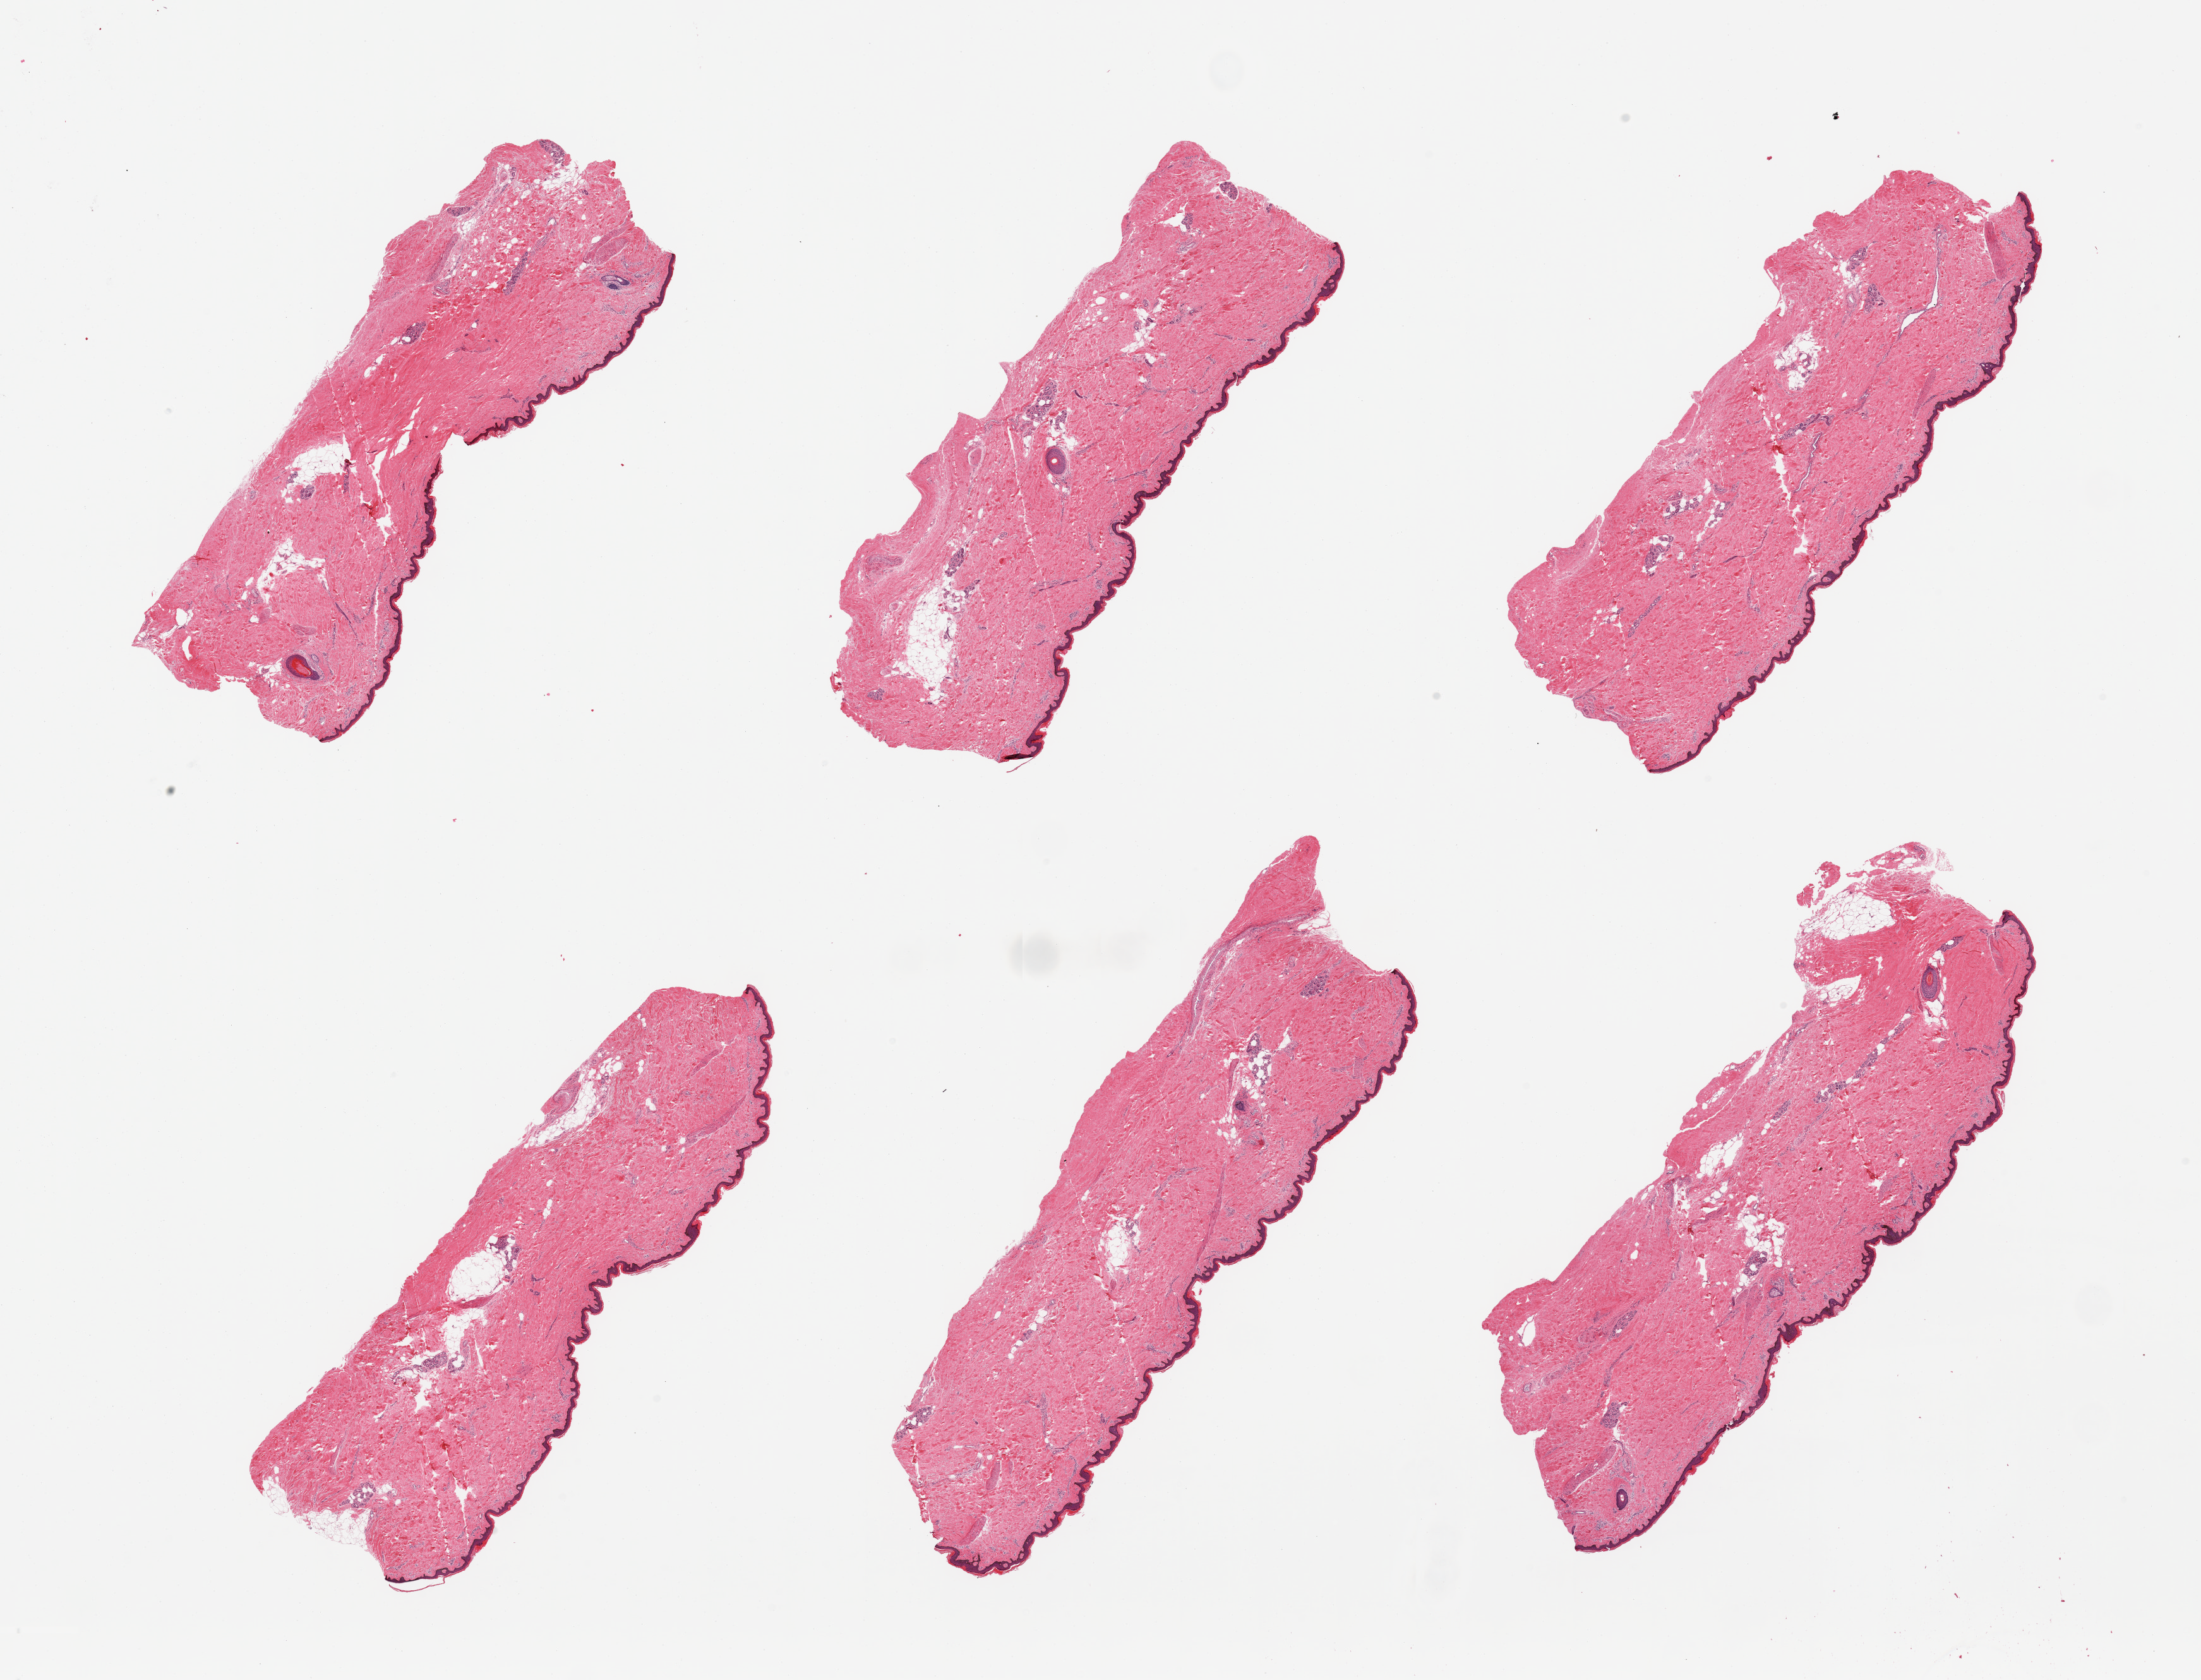
Whole-slide image, haematoxylin and eosin stain, brightfield, shown as a low-resolution overview of the whole scanned area (about 27.6 x 21.0 mm, acquisition: 20x scan). PAXgene-fixed, paraffin-embedded tissue. Target tissue: skin of lower leg. Tissue donor sample.
* pathologist's review note for this sample: 6 pieces; well trimmed; 10% dermal fat